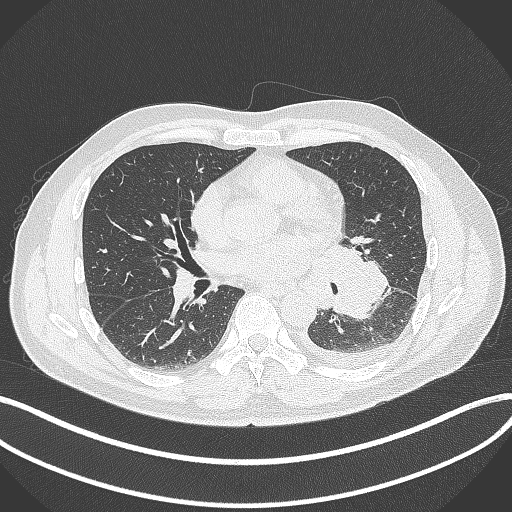
Chest CT, one axial slice; slice 177 of 342 in the series (ordered by position); reconstruction kernel B70f; 120 kVp; lung window (W 1500 / L -600 HU); 1 mm slice thickness; 512 × 512 image matrix, field of view 400 × 400 mm. Patient: male, 58 years. From the clinical record (not read from this slice): clinical TNM (as recorded): T3 N1 M1b; histopathological grade: G3.
Annotated regions visible in this slice (bounding box drawn by a radiologist):
- lung tumour (recorded histology: small cell carcinoma): box from (x=316, y=236) to (x=395, y=321) px